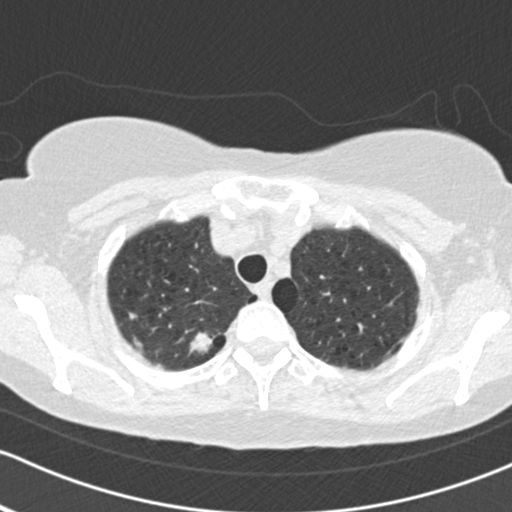
Chest CT (low-dose screening protocol), one axial image; second screening round (one year after baseline); lung window (W 1500 / L -600 HU); slice 21 of 161 in the series; 512 × 512 image matrix, field of view 312 × 312 mm. Female participant, aged 64 years at enrolment. Current smoker at enrolment.
Expert reader's lesion annotation, box from (x=172, y=322) to (x=226, y=372) px. The exam's reader record, not a measurement of the box and not confirmed to be the same lesion: non-calcified nodule or mass ≥4 mm, right upper lobe, 16 × 15 mm, spiculated (stellate) margins, soft tissue attenuation, pre-existing on the prior screen: no. Official screen result: positive, other. Lung cancer was diagnosed 45 days after this screen: adenocarcinoma, NOS, right upper lobe, poorly differentiated (G3), stage IB (AJCC 6th edition), 15 mm at pathology.